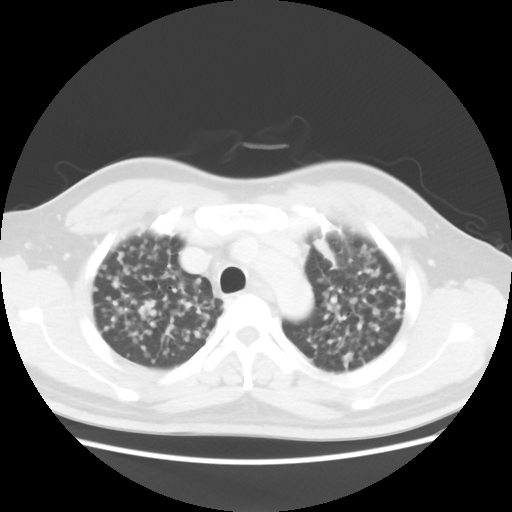
Chest CT, one axial slice; slice 31 of 40 in the series (ordered by position); reconstruction kernel STANDARD; lung window (W 1500 / L -600 HU); 512 × 512 image matrix. Patient: male, 41 years. Case-level facts recorded for this patient, not image findings: clinical TNM (as recorded): T1c N3 M1b; histopathological grade: G2-3.
Outlined on this slice (rectangle marked by the reading radiologist):
- lung tumour (recorded histology: adenocarcinoma): bounding box <315,236,337,268> (left, top, right, bottom; pixels)